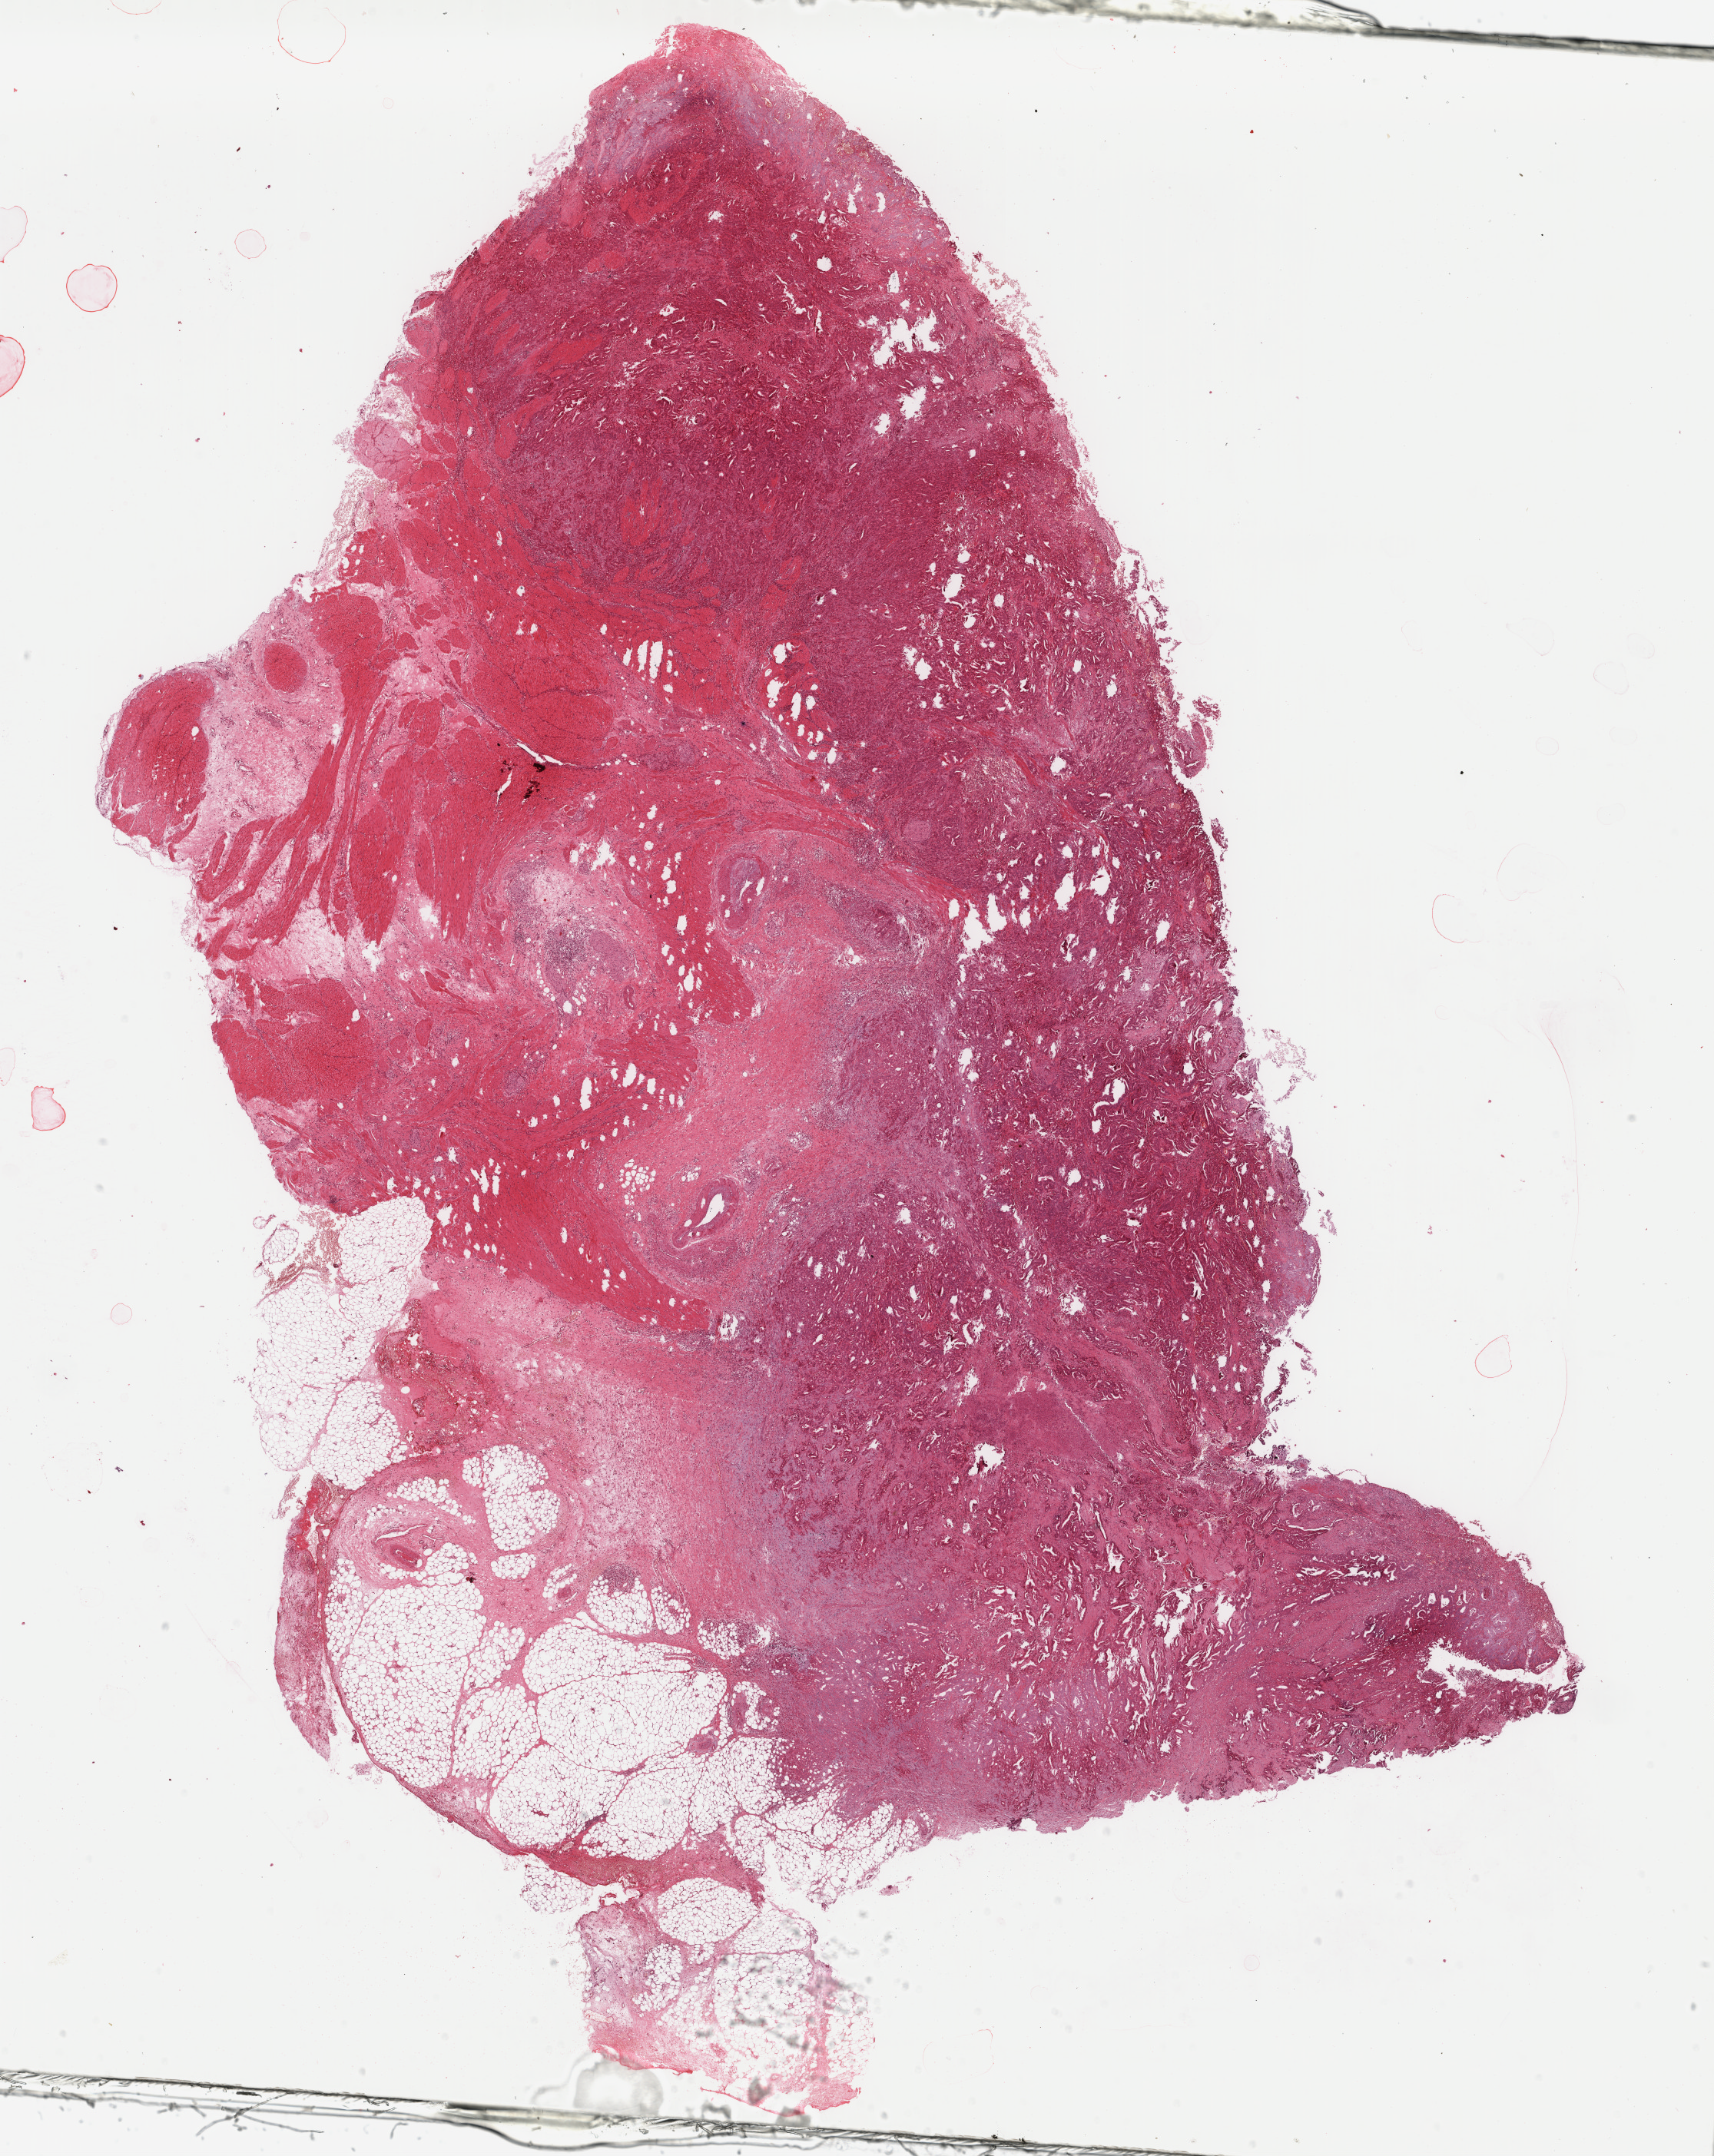
Whole-slide histology image, Hematoxylin and eosin (H&E) stained, low-resolution overview of the scanned area, about 17.7 x 22.3 mm (from a 40x scan); formalin-fixed paraffin-embedded (FFPE) diagnostic section; sample: primary tumour, stomach. Male, age 60 years at initial diagnosis. Histologic grade: G2 (moderately differentiated).
- AJCC pathologic stage: IB (7th edition)
- TNM: T2 N0 M0
- pathologic diagnosis: Adenocarcinoma, NOS (fundus of stomach)